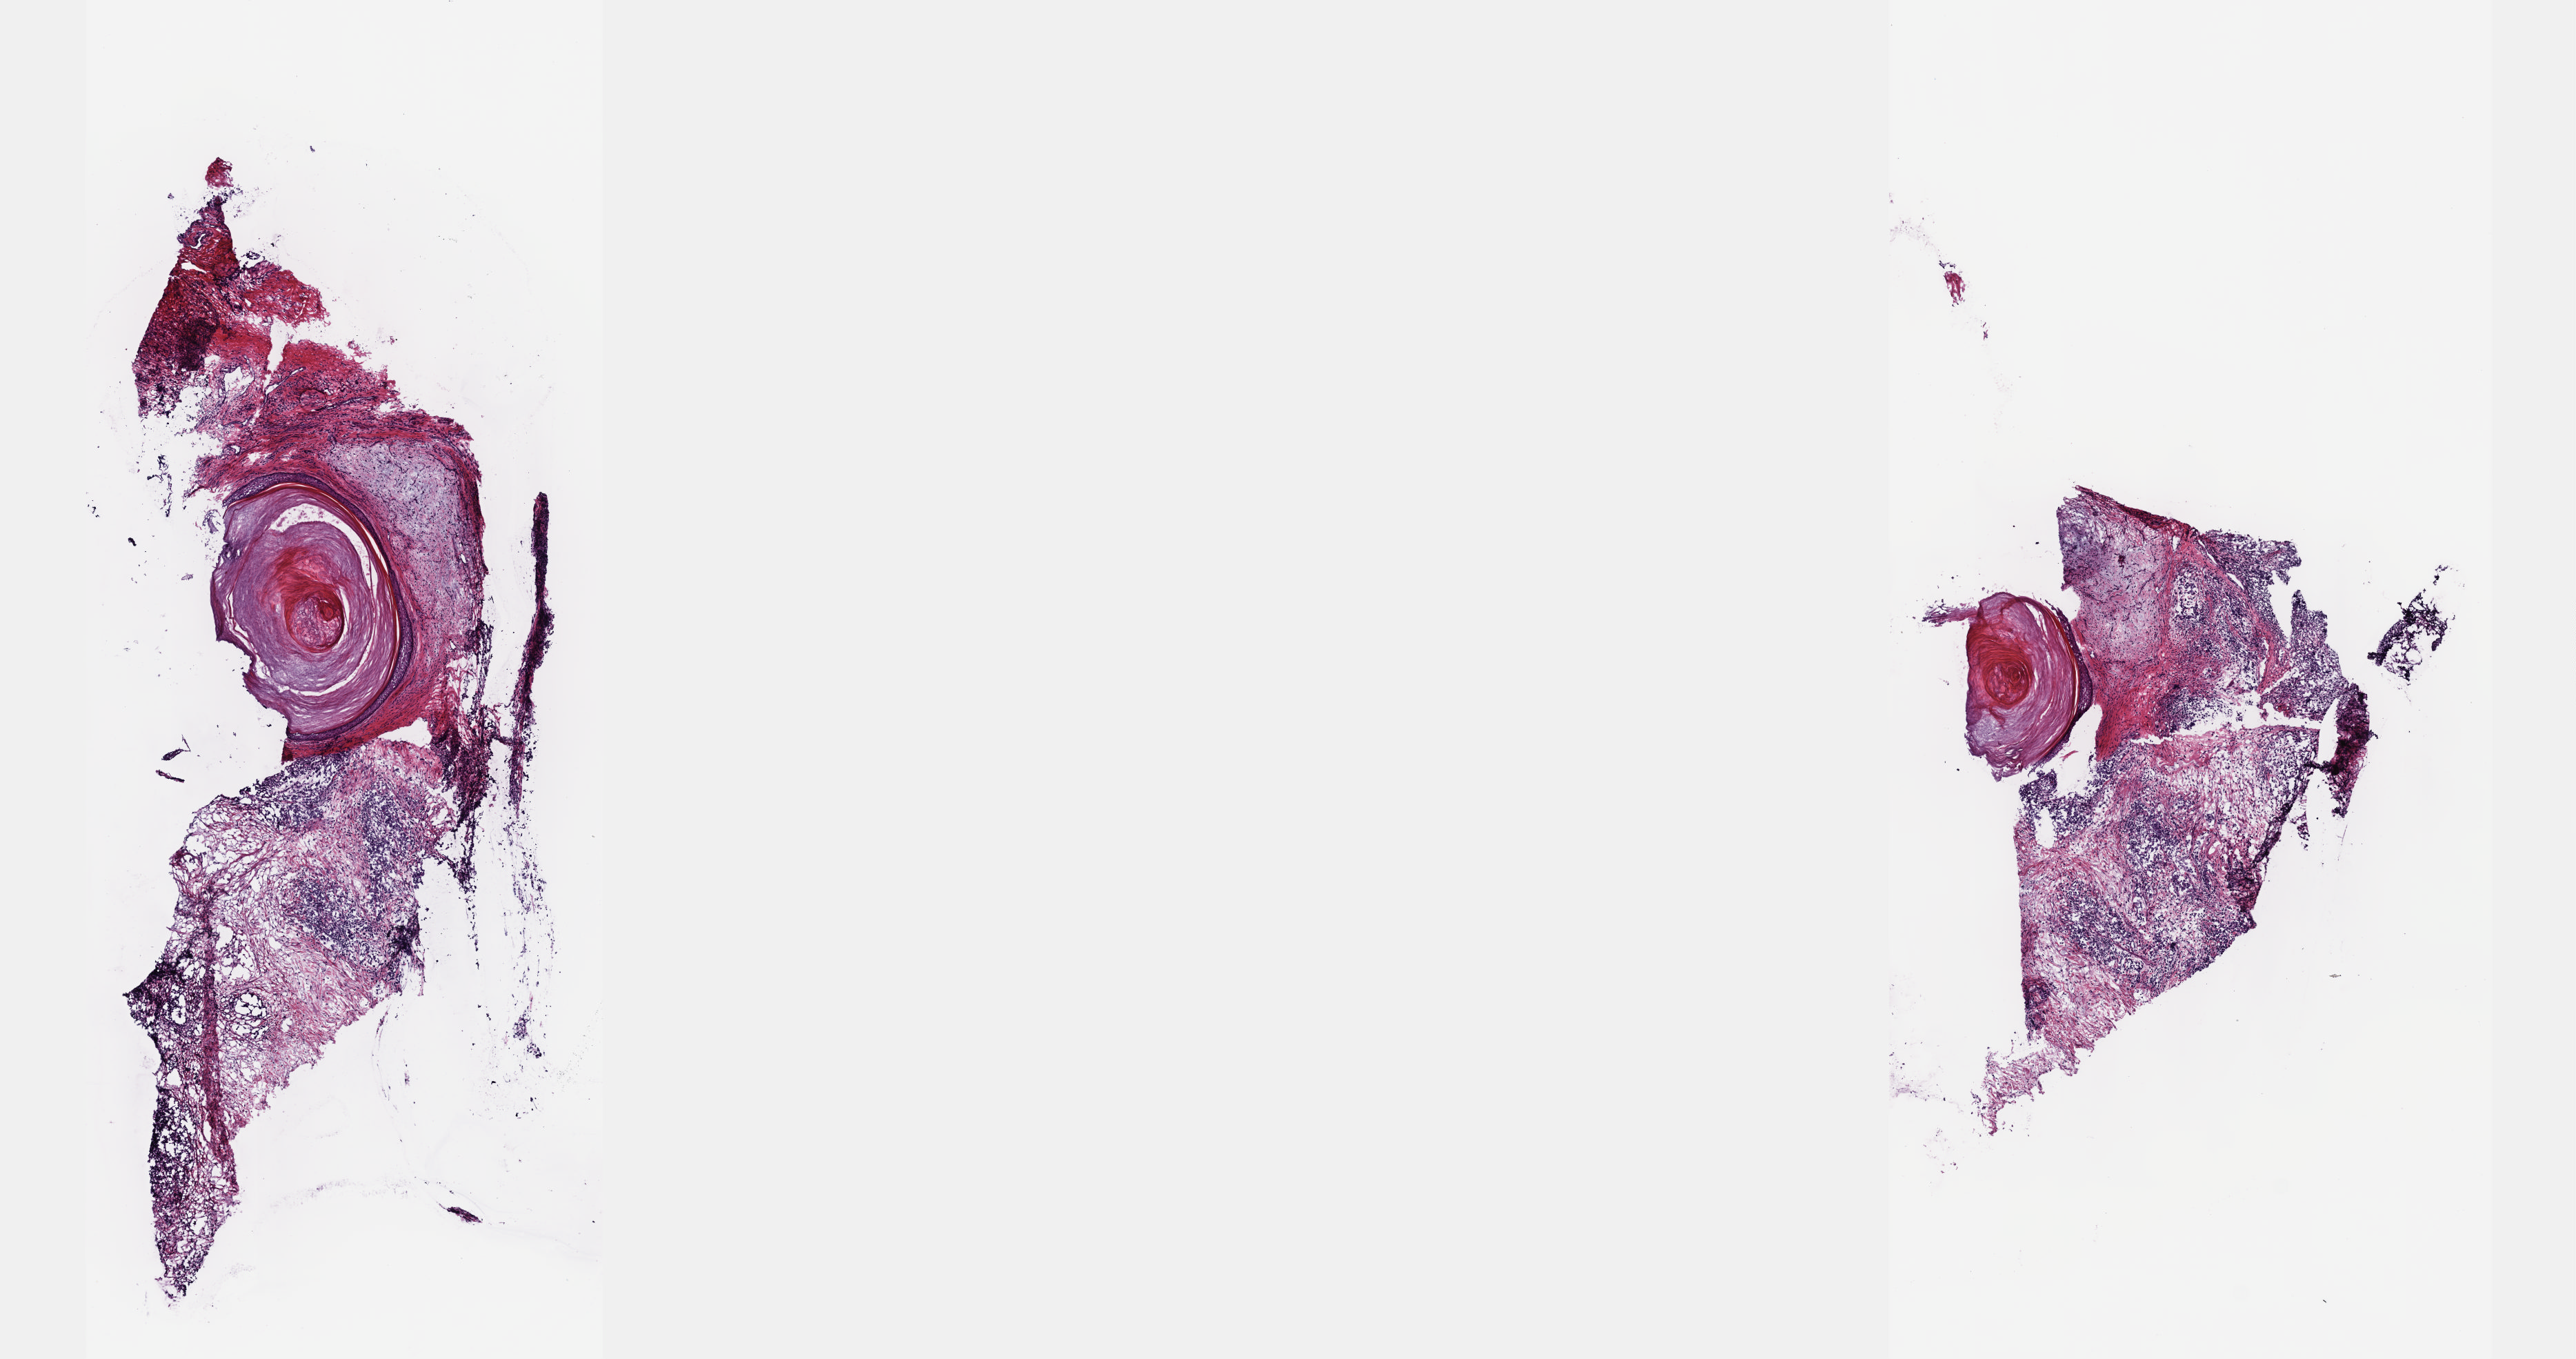
H&E whole-slide image, shown as a low-resolution overview of the whole scanned area (about 15.1 x 8.0 mm); frozen section; primary tumour sample from the testis. Patient: male, age at initial diagnosis 21 years. Pathologist review of this section (percent, as recorded): tumour cells 100%, tumour nuclei 100%, normal cells 0%, stromal cells 0%, necrosis 0%. Infiltration values recorded for this section: lymphocyte infiltration 0%, monocyte infiltration 0%, neutrophil infiltration 0%.
AJCC pathologic stage: IS (7th edition). Pathologic diagnosis: Mixed germ cell tumor. TNM: T2 NX M0.